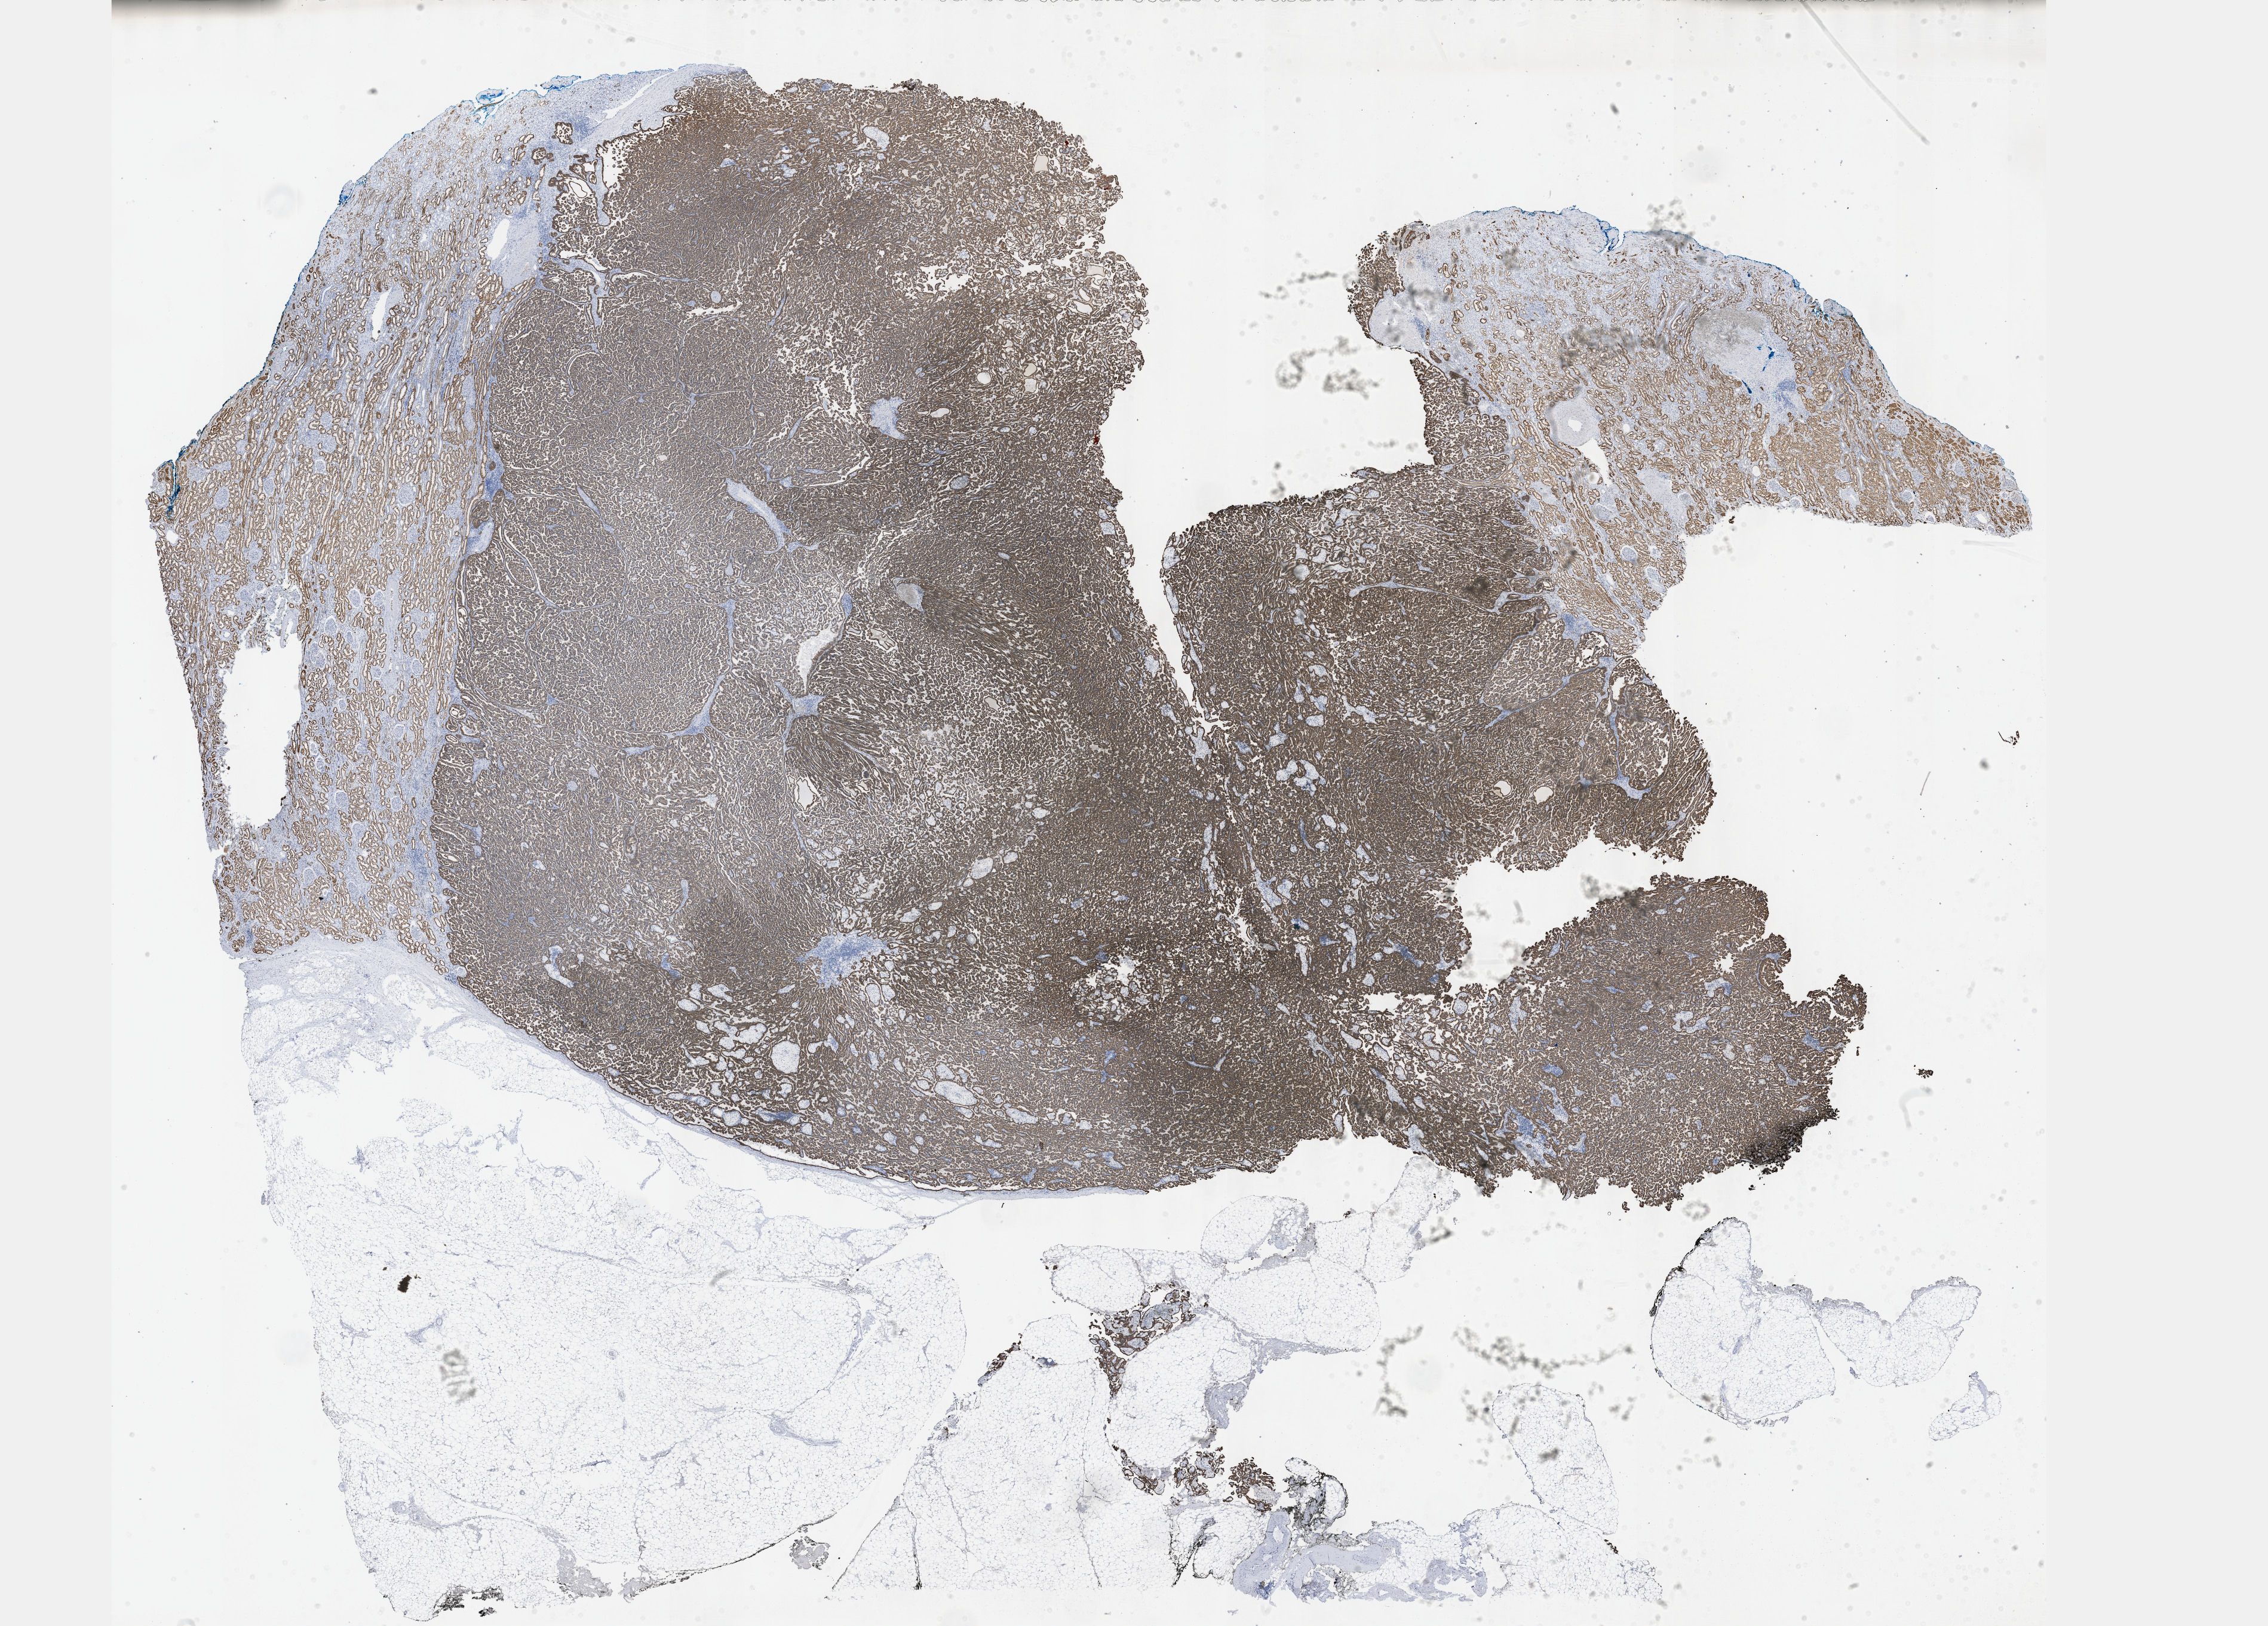
H&E whole-slide image, a low-resolution overview of the entire scanned area, about 30.7 x 22.0 mm; formalin-fixed paraffin-embedded (FFPE) diagnostic section; kidney, primary tumour sample. Male patient; age at initial diagnosis 65 years.
Histologic diagnosis: Papillary adenocarcinoma, NOS. AJCC pathologic stage: I (7th edition). TNM: T1a NX MX.